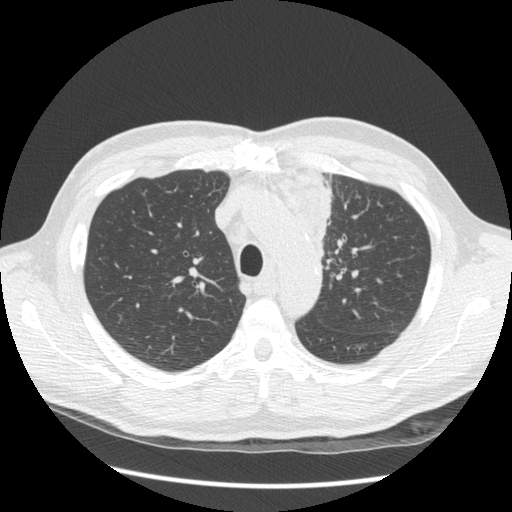
Low-dose screening chest CT, one axial slice; slice 104 of 136 in the series (ordered by position); lung window (W 1500 / L -600 HU); 2.5 mm slice thickness; 512 × 512 image matrix, field of view 360 × 360 mm.
Structures marked on this image (manually delineated by an expert):
- lesion 1 (tumor, upper lobe of left lung): box from (x=282, y=167) to (x=331, y=256) px